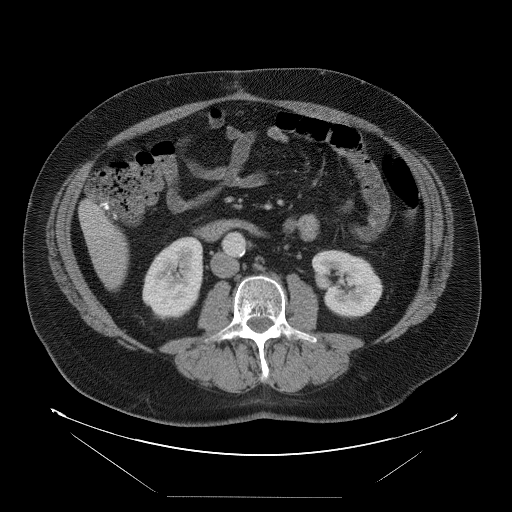
Contrast-enhanced abdominal CT, one axial slice; slice 20 of 114 in the series (ordered by position); intravenous contrast given; soft-tissue window (W 400 / L 40 HU); 5 mm slice thickness; 512 × 512 image matrix, field of view 500 × 500 mm. Male patient, age 61 years. Case-level facts recorded for this patient, not image findings: diagnosis: colorectal cancer liver metastases, imaged before liver resection; multiple liver metastases: no; largest metastasis: 6.5 cm; disease in both lobes: yes.
Outlined on this slice (outlined manually by an expert reader):
- liver: box from (x=81, y=202) to (x=129, y=290) px